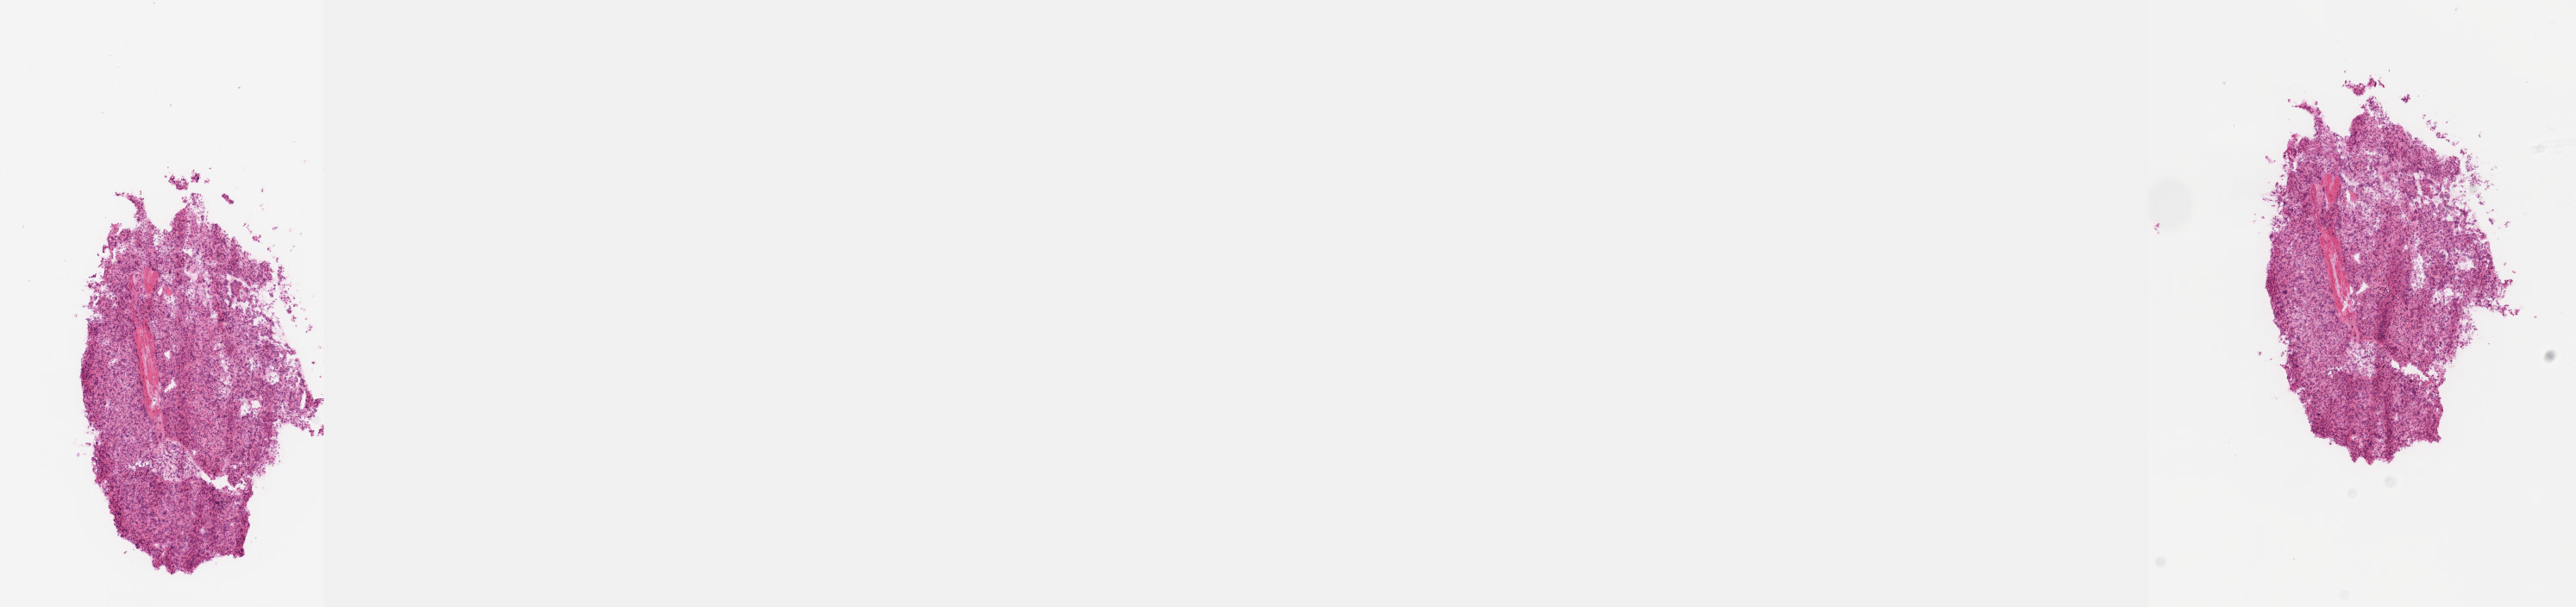
Whole-slide histology image, H&E-stained — a low-resolution overview of the entire scanned area, about 24.1 x 5.7 mm (from a 20x scan). Frozen section from the top of the tissue portion. Sample: primary tumour, retroperitoneum and peritoneum. Male, age 30 years at initial diagnosis. Slide review estimates, as recorded: tumour cells 80%, tumour nuclei 80%, normal cells 0%, stromal cells 20%, necrosis 0%. Infiltration values recorded for this section: lymphocyte infiltration 2%, monocyte infiltration 1%, neutrophil infiltration 1%.
• diagnosis: Extra-adrenal paraganglioma, NOS (retroperitoneum)